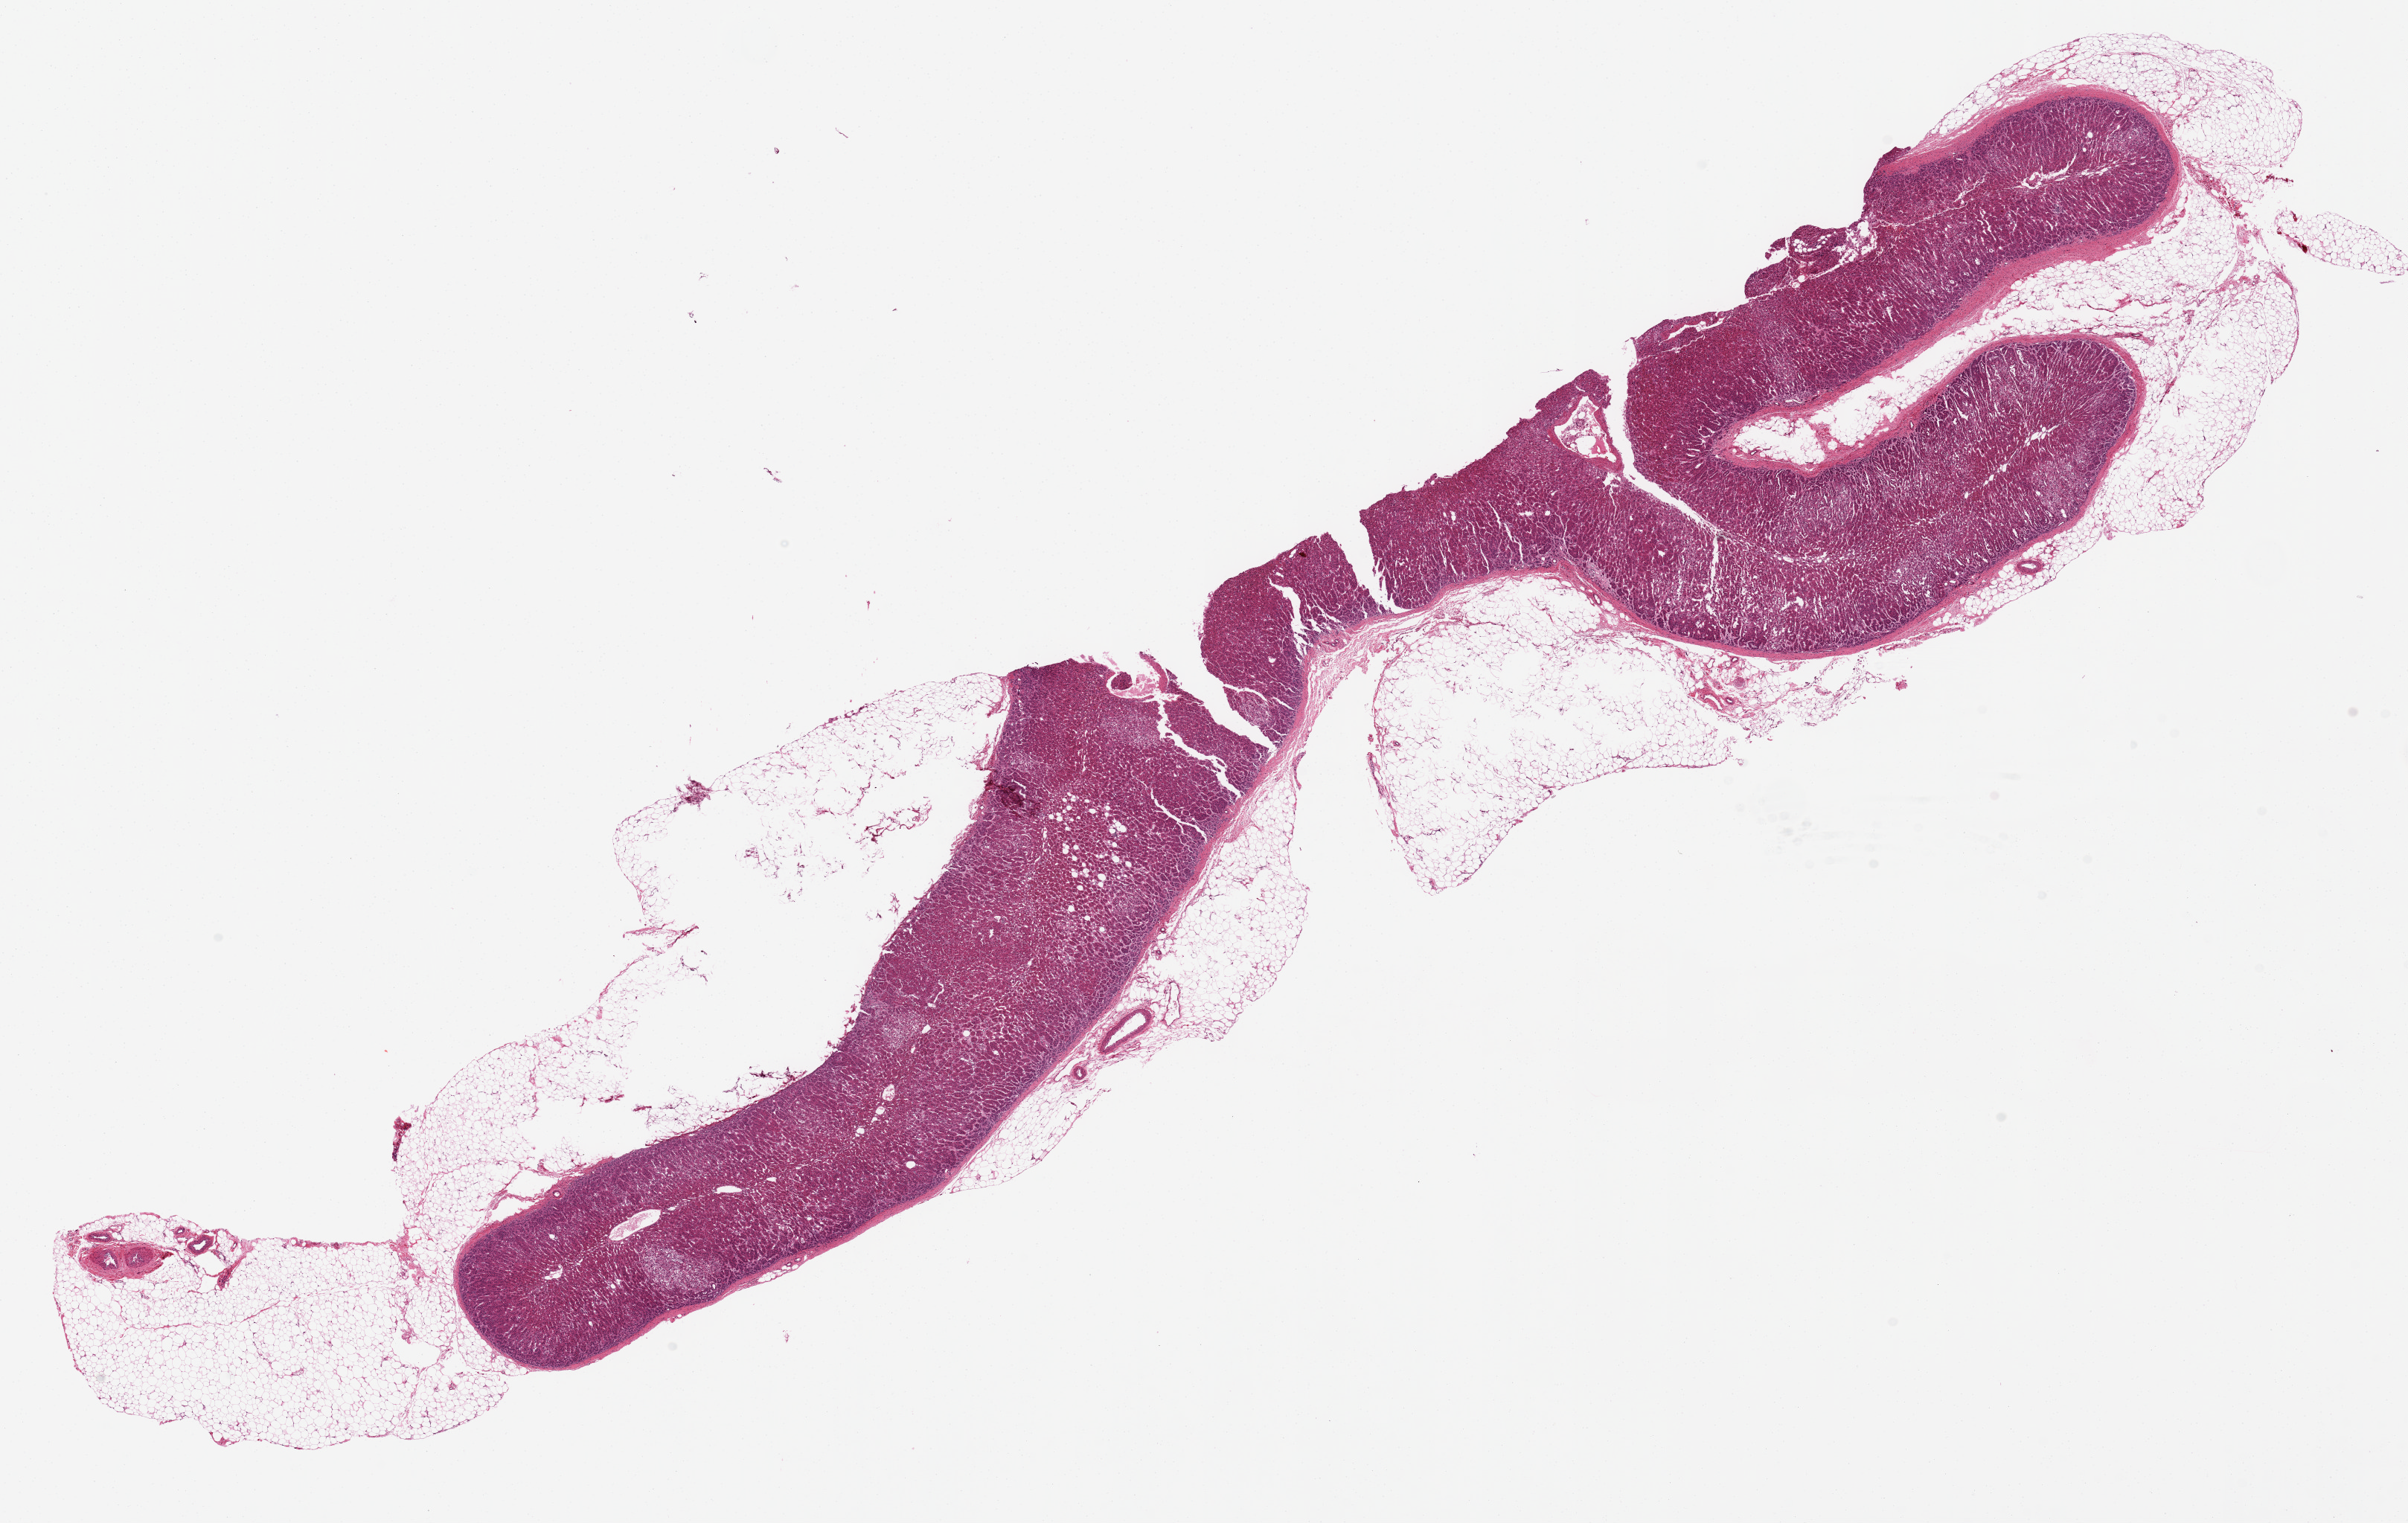
Digitized H&E-stained section, brightfield — shown as a low-resolution overview of the whole scanned area (about 25.6 x 16.2 mm, slide scanned at 20x); PAXgene-fixed, paraffin-embedded tissue; target tissue: adrenal gland; tissue donor sample. Male donor.
- reviewer comment on this tissue sample: 21x4 mm. Abundant well preserved cortex